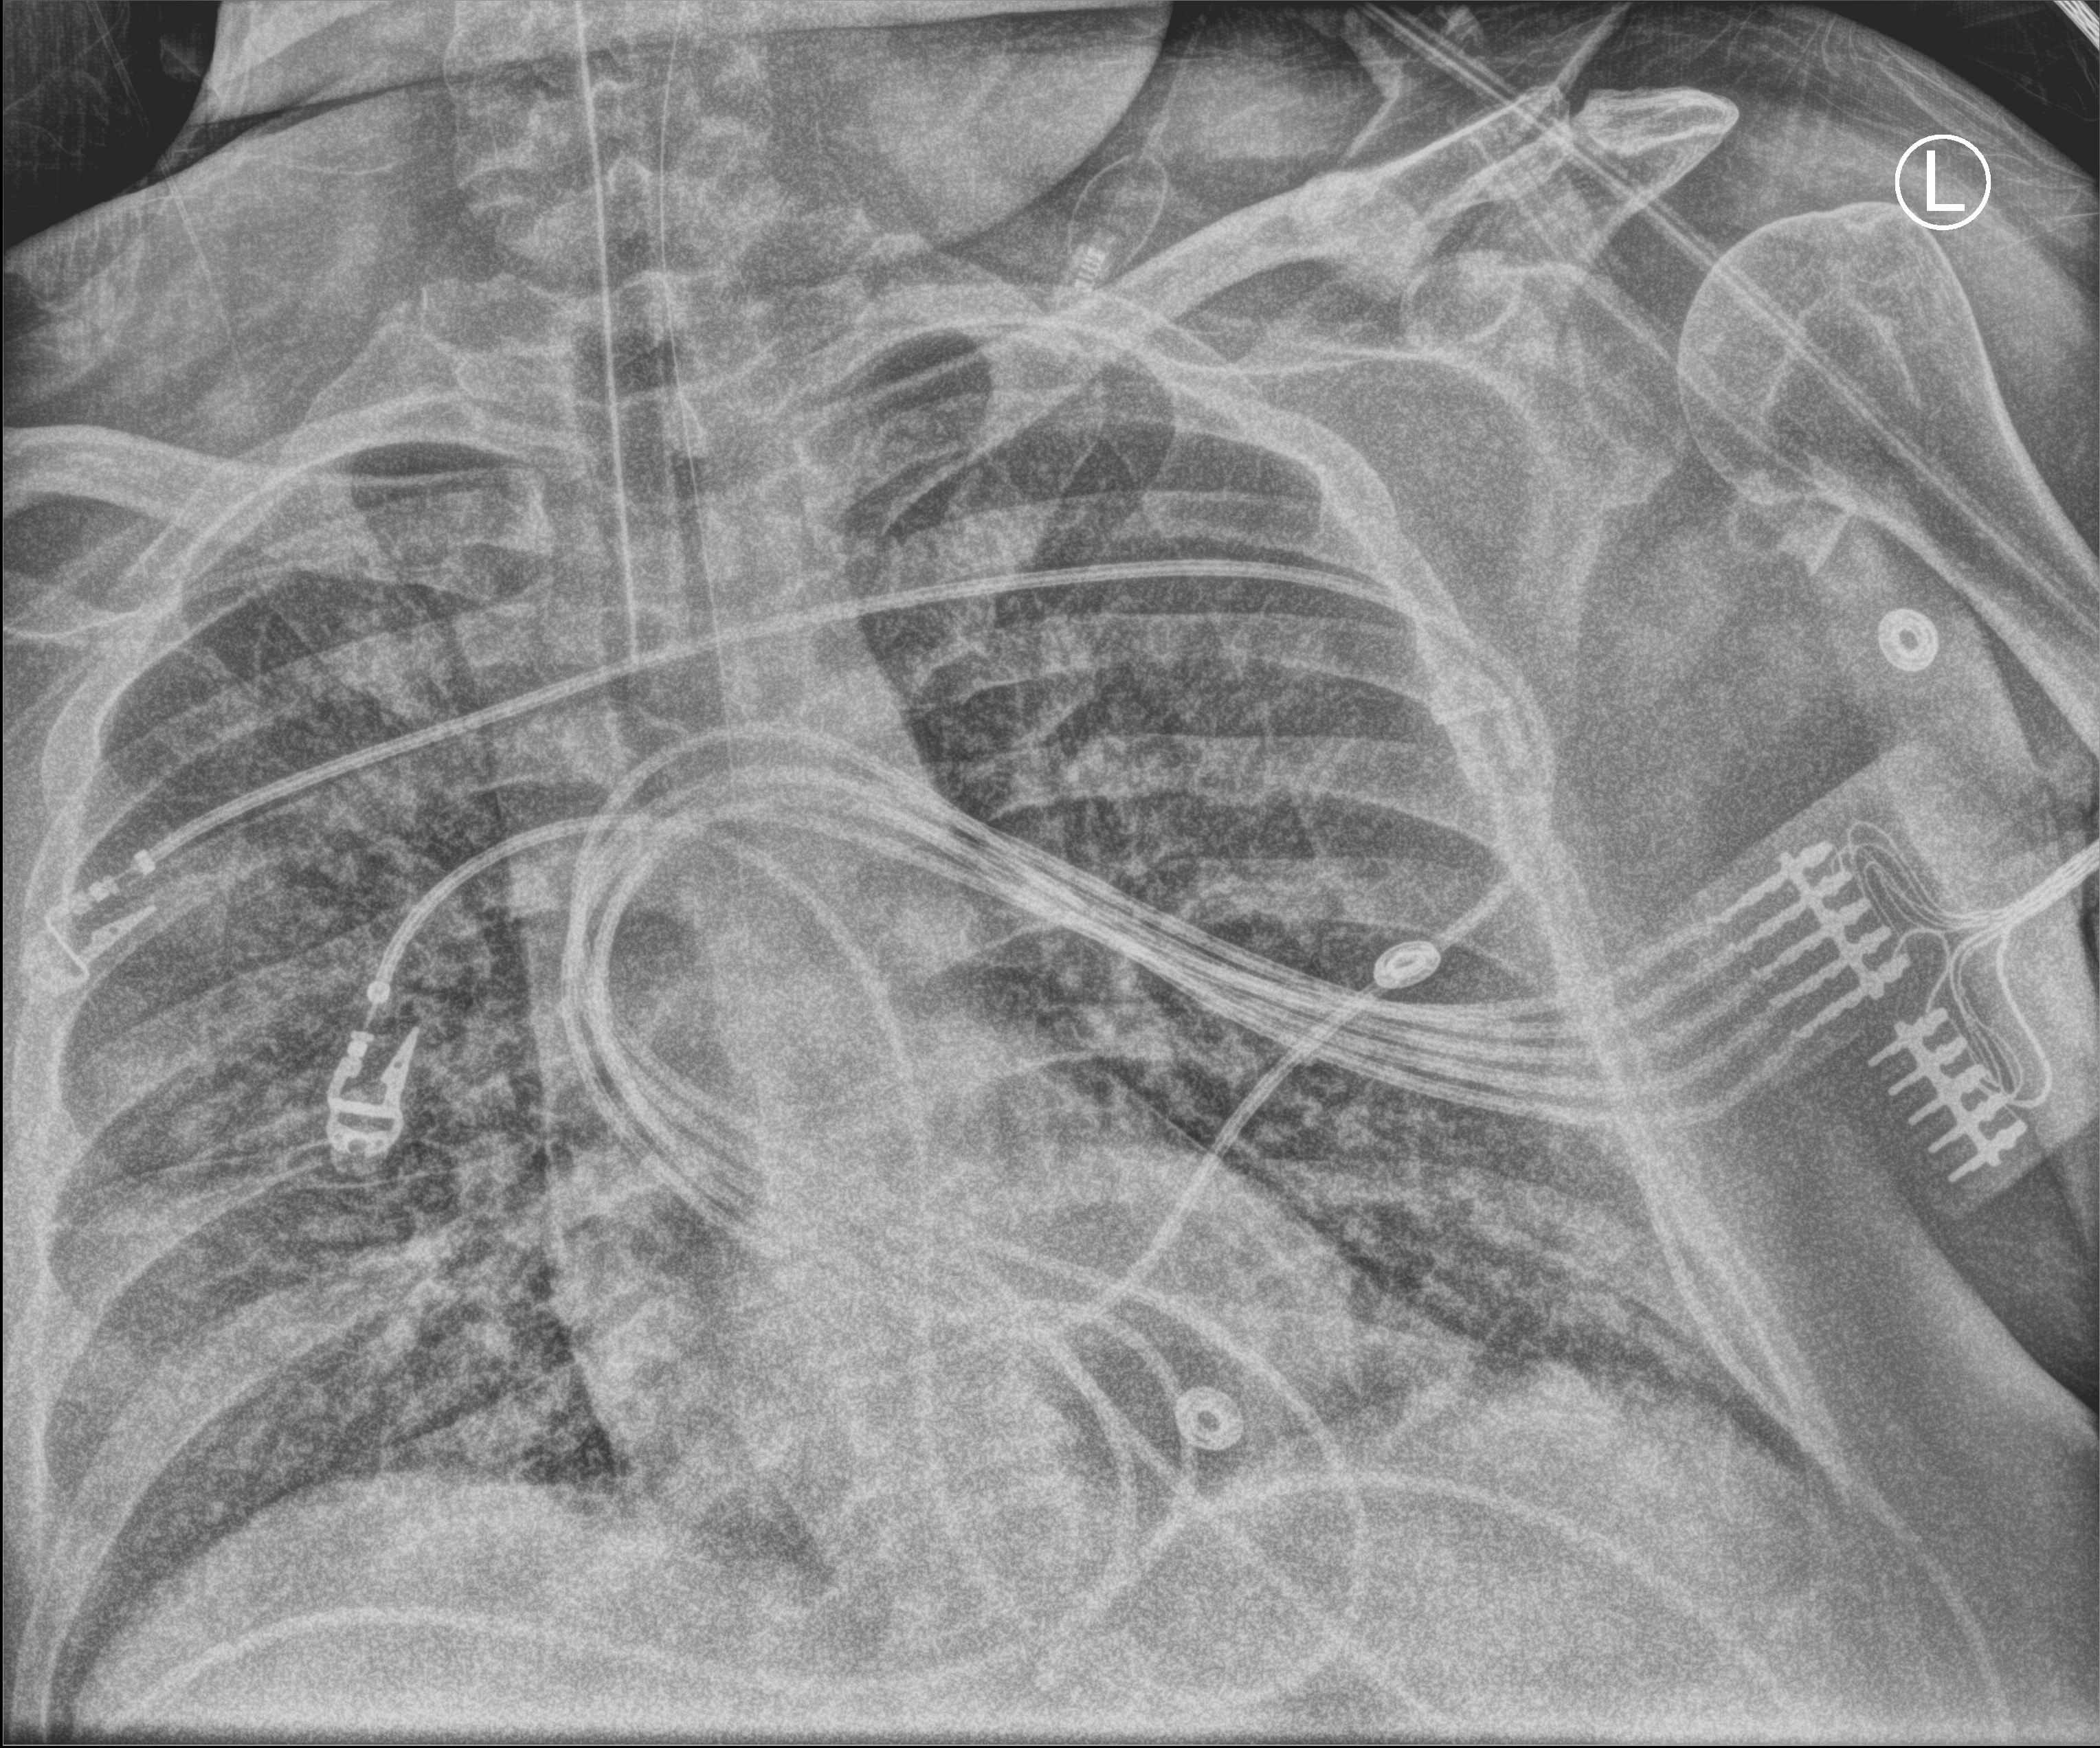
Portable chest radiograph. Patient hospitalised with COVID-19, aged 18–59 years.
From the hospital-stay record, not from the radiograph (when in the stay this image was taken is not recorded): chronic kidney disease (admission record): no.